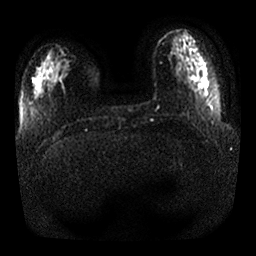
Breast MRI, one axial slice; position 7 of 25 along the scan axis; diffusion-weighted series; image 2 of 4 stored at this slice position (different b-values; order by instance number); 1.5 T; 4 mm slice thickness; 256 × 256 image matrix, field of view 350 × 350 mm. Female patient.
Structures marked on this image (expert manual segmentation):
- tumour on diffusion-weighted imaging: box from (x=55, y=61) to (x=68, y=74) px